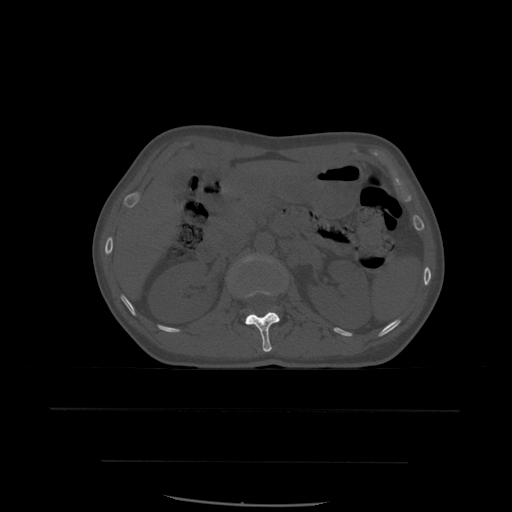
CT including the spine, one axial slice; slice 242 of 574 in the series (ordered by position); bone window (W 1800 / L 400 HU); 1.25 mm slice thickness; 512 × 512 image matrix, field of view 392 × 392 mm. Patient age 48 years. From the clinical record (not read from this slice): primary cancer: lung.
Annotated regions visible in this slice (semi-automatic segmentation, software-assisted and operator-edited):
- L1 vertebra: bounding box <244,288,284,352> (left, top, right, bottom; pixels)
- L2 vertebra: <240,256,273,264>